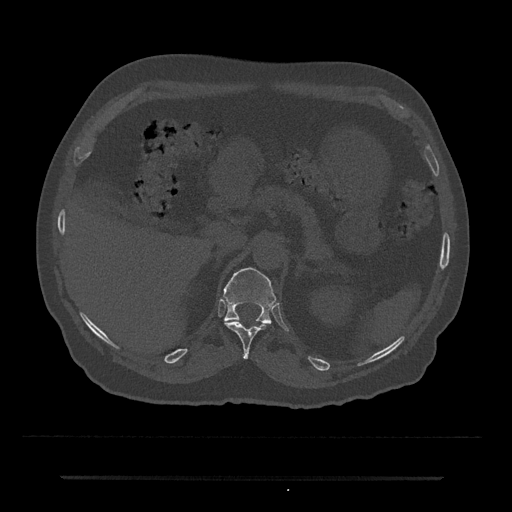
CT including the spine, one axial slice. Position 153 of 797 along the scan axis. 120 kVp. Bone window (W 1800 / L 400 HU). 0.5 mm slice thickness. 512 × 512 image matrix, field of view 437 × 437 mm. Patient: male, 69 years. Case-level facts recorded for this patient, not image findings: primary cancer: prostate.
Annotated regions visible in this slice (semi-automatically segmented with operator editing):
- T11 vertebra: bounding box <225,321,266,359> (left, top, right, bottom; pixels)
- T12 vertebra: <223,267,276,325>